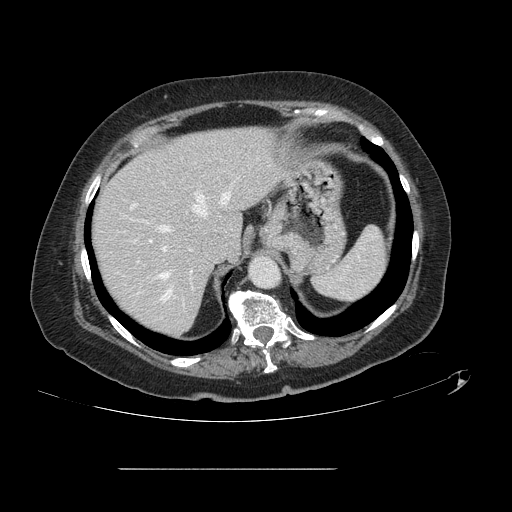
Contrast-enhanced abdominal CT, one axial slice. 120 kVp. Intravenous contrast given. Soft-tissue window (W 400 / L 40 HU). 2.5 mm slice thickness. 512 × 512 image matrix, field of view 439 × 439 mm. Female patient, age 75 years. Case-level facts recorded for this patient, not image findings: diagnosis: colorectal cancer liver metastases, imaged before liver resection; multiple liver metastases: no; largest metastasis: 2.4 cm; disease in both lobes: no.
Structures marked on this image (expert manual segmentation):
- hepatic veins: box from (x=158, y=182) to (x=234, y=300) px
- liver: (x=92, y=127)–(x=283, y=336)
- planned liver remnant (the part of the liver to remain after resection): (x=92, y=127)–(x=283, y=336)
- portal vein (with intrahepatic branches): (x=134, y=205)–(x=166, y=251)